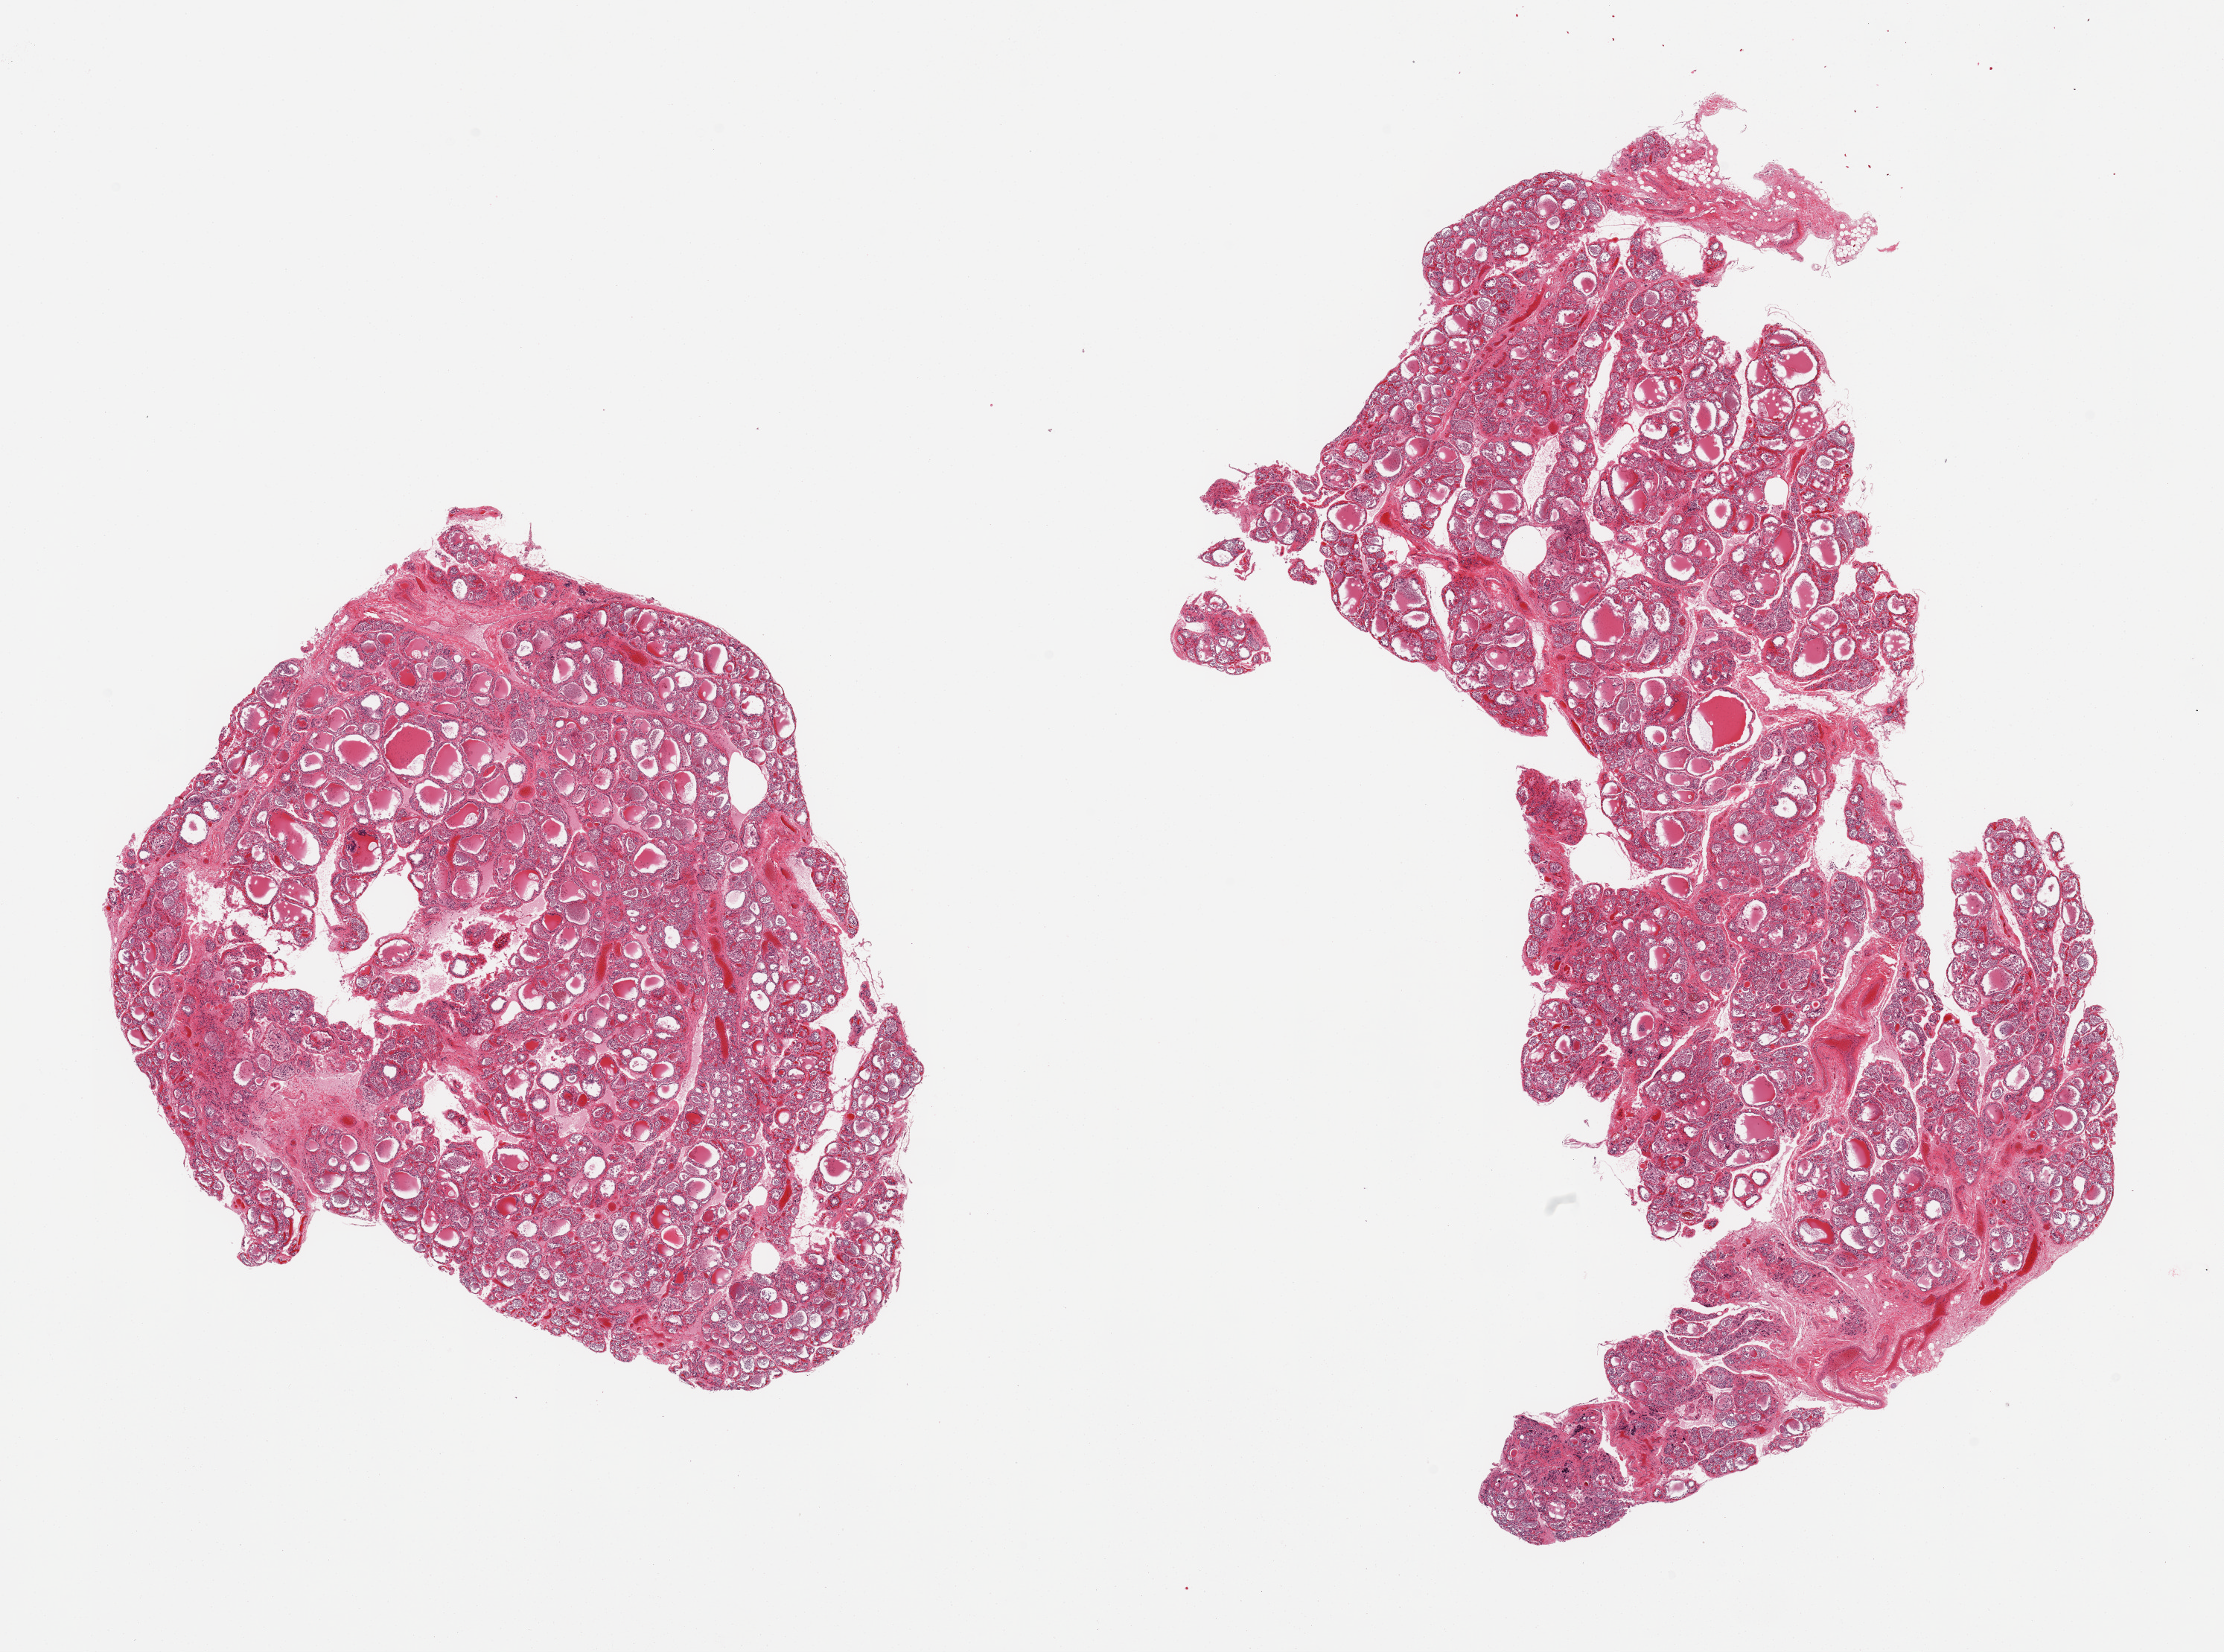
Whole-slide image, haematoxylin and eosin stain, brightfield — shown as a low-resolution overview of the whole scanned area (about 23.6 x 17.6 mm, slide scanned at 20x). PAXgene-fixed paraffin-embedded (PFPE) section. Sampled site (target tissue): thyroid. Tissue donor sample.
Pathologist's review note for this sample: 2 pieces; some nodularity and regressive change.